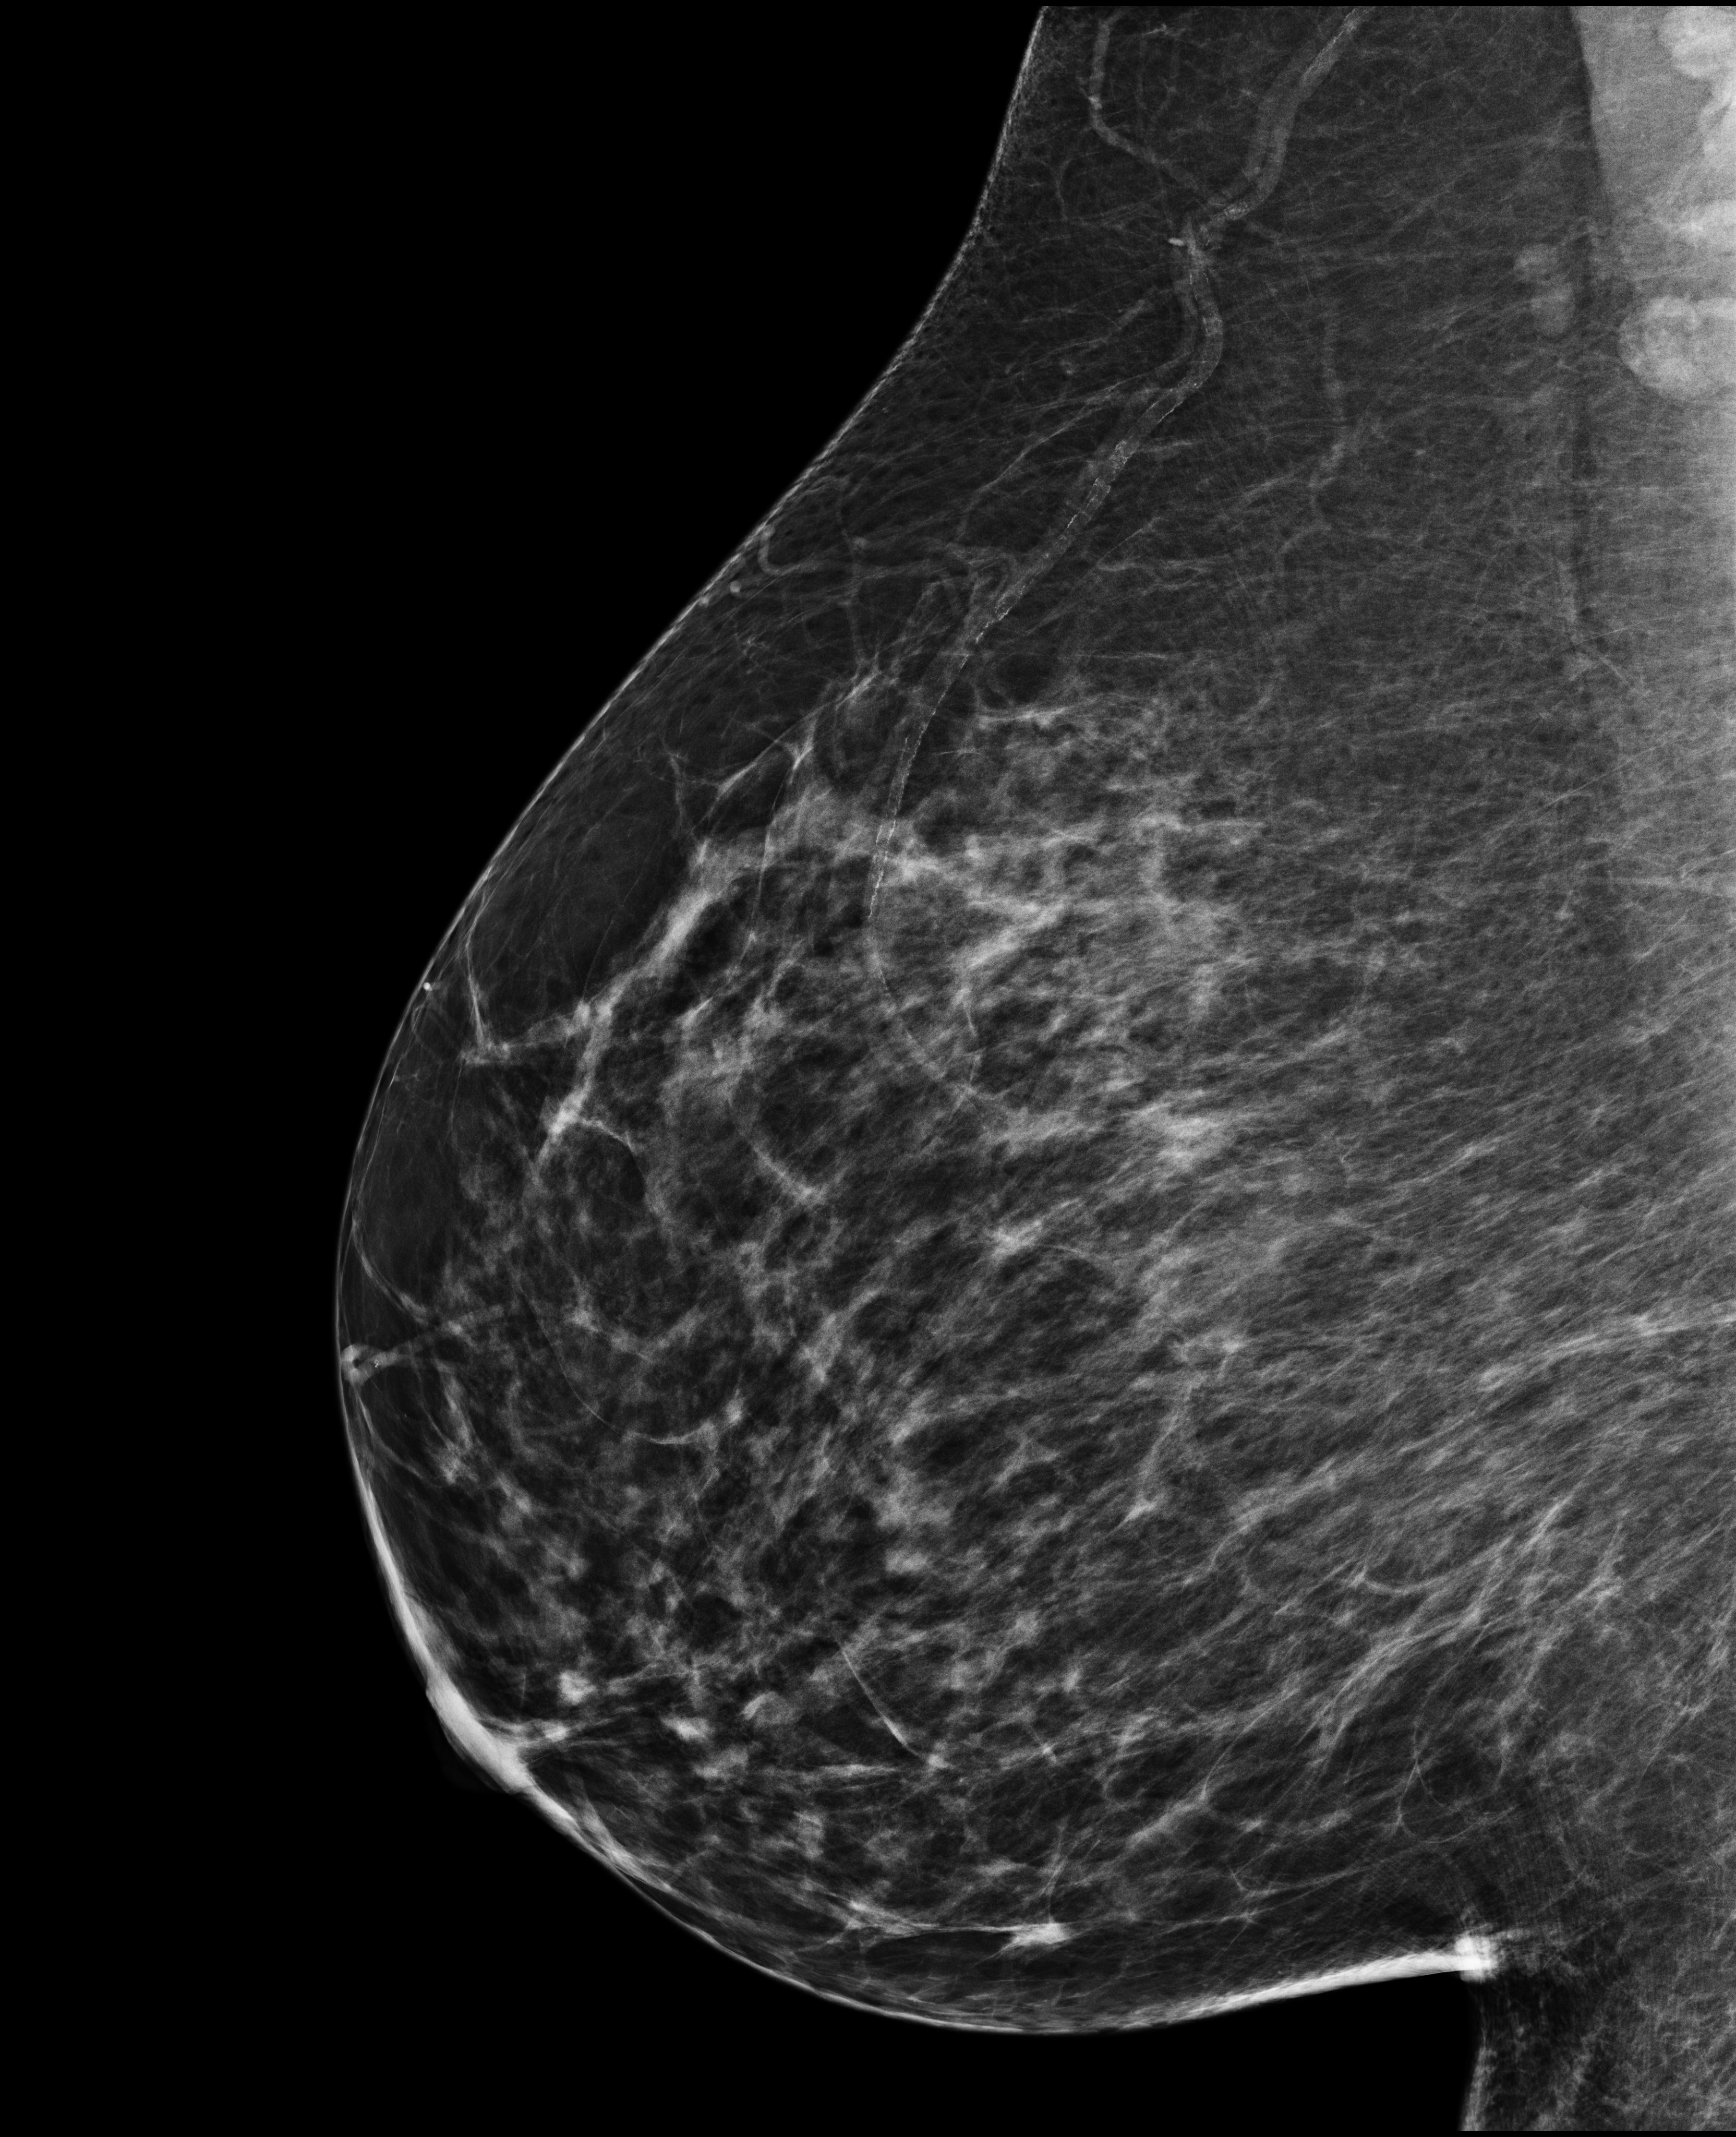
Annual screening mammography examination; compressed breast thickness 87 mm; system: Selenia Dimensions. Patient aged 68 years (female).
Image type: full-field digital mammogram. Breast: right. Projection: mediolateral oblique (MLO) view.